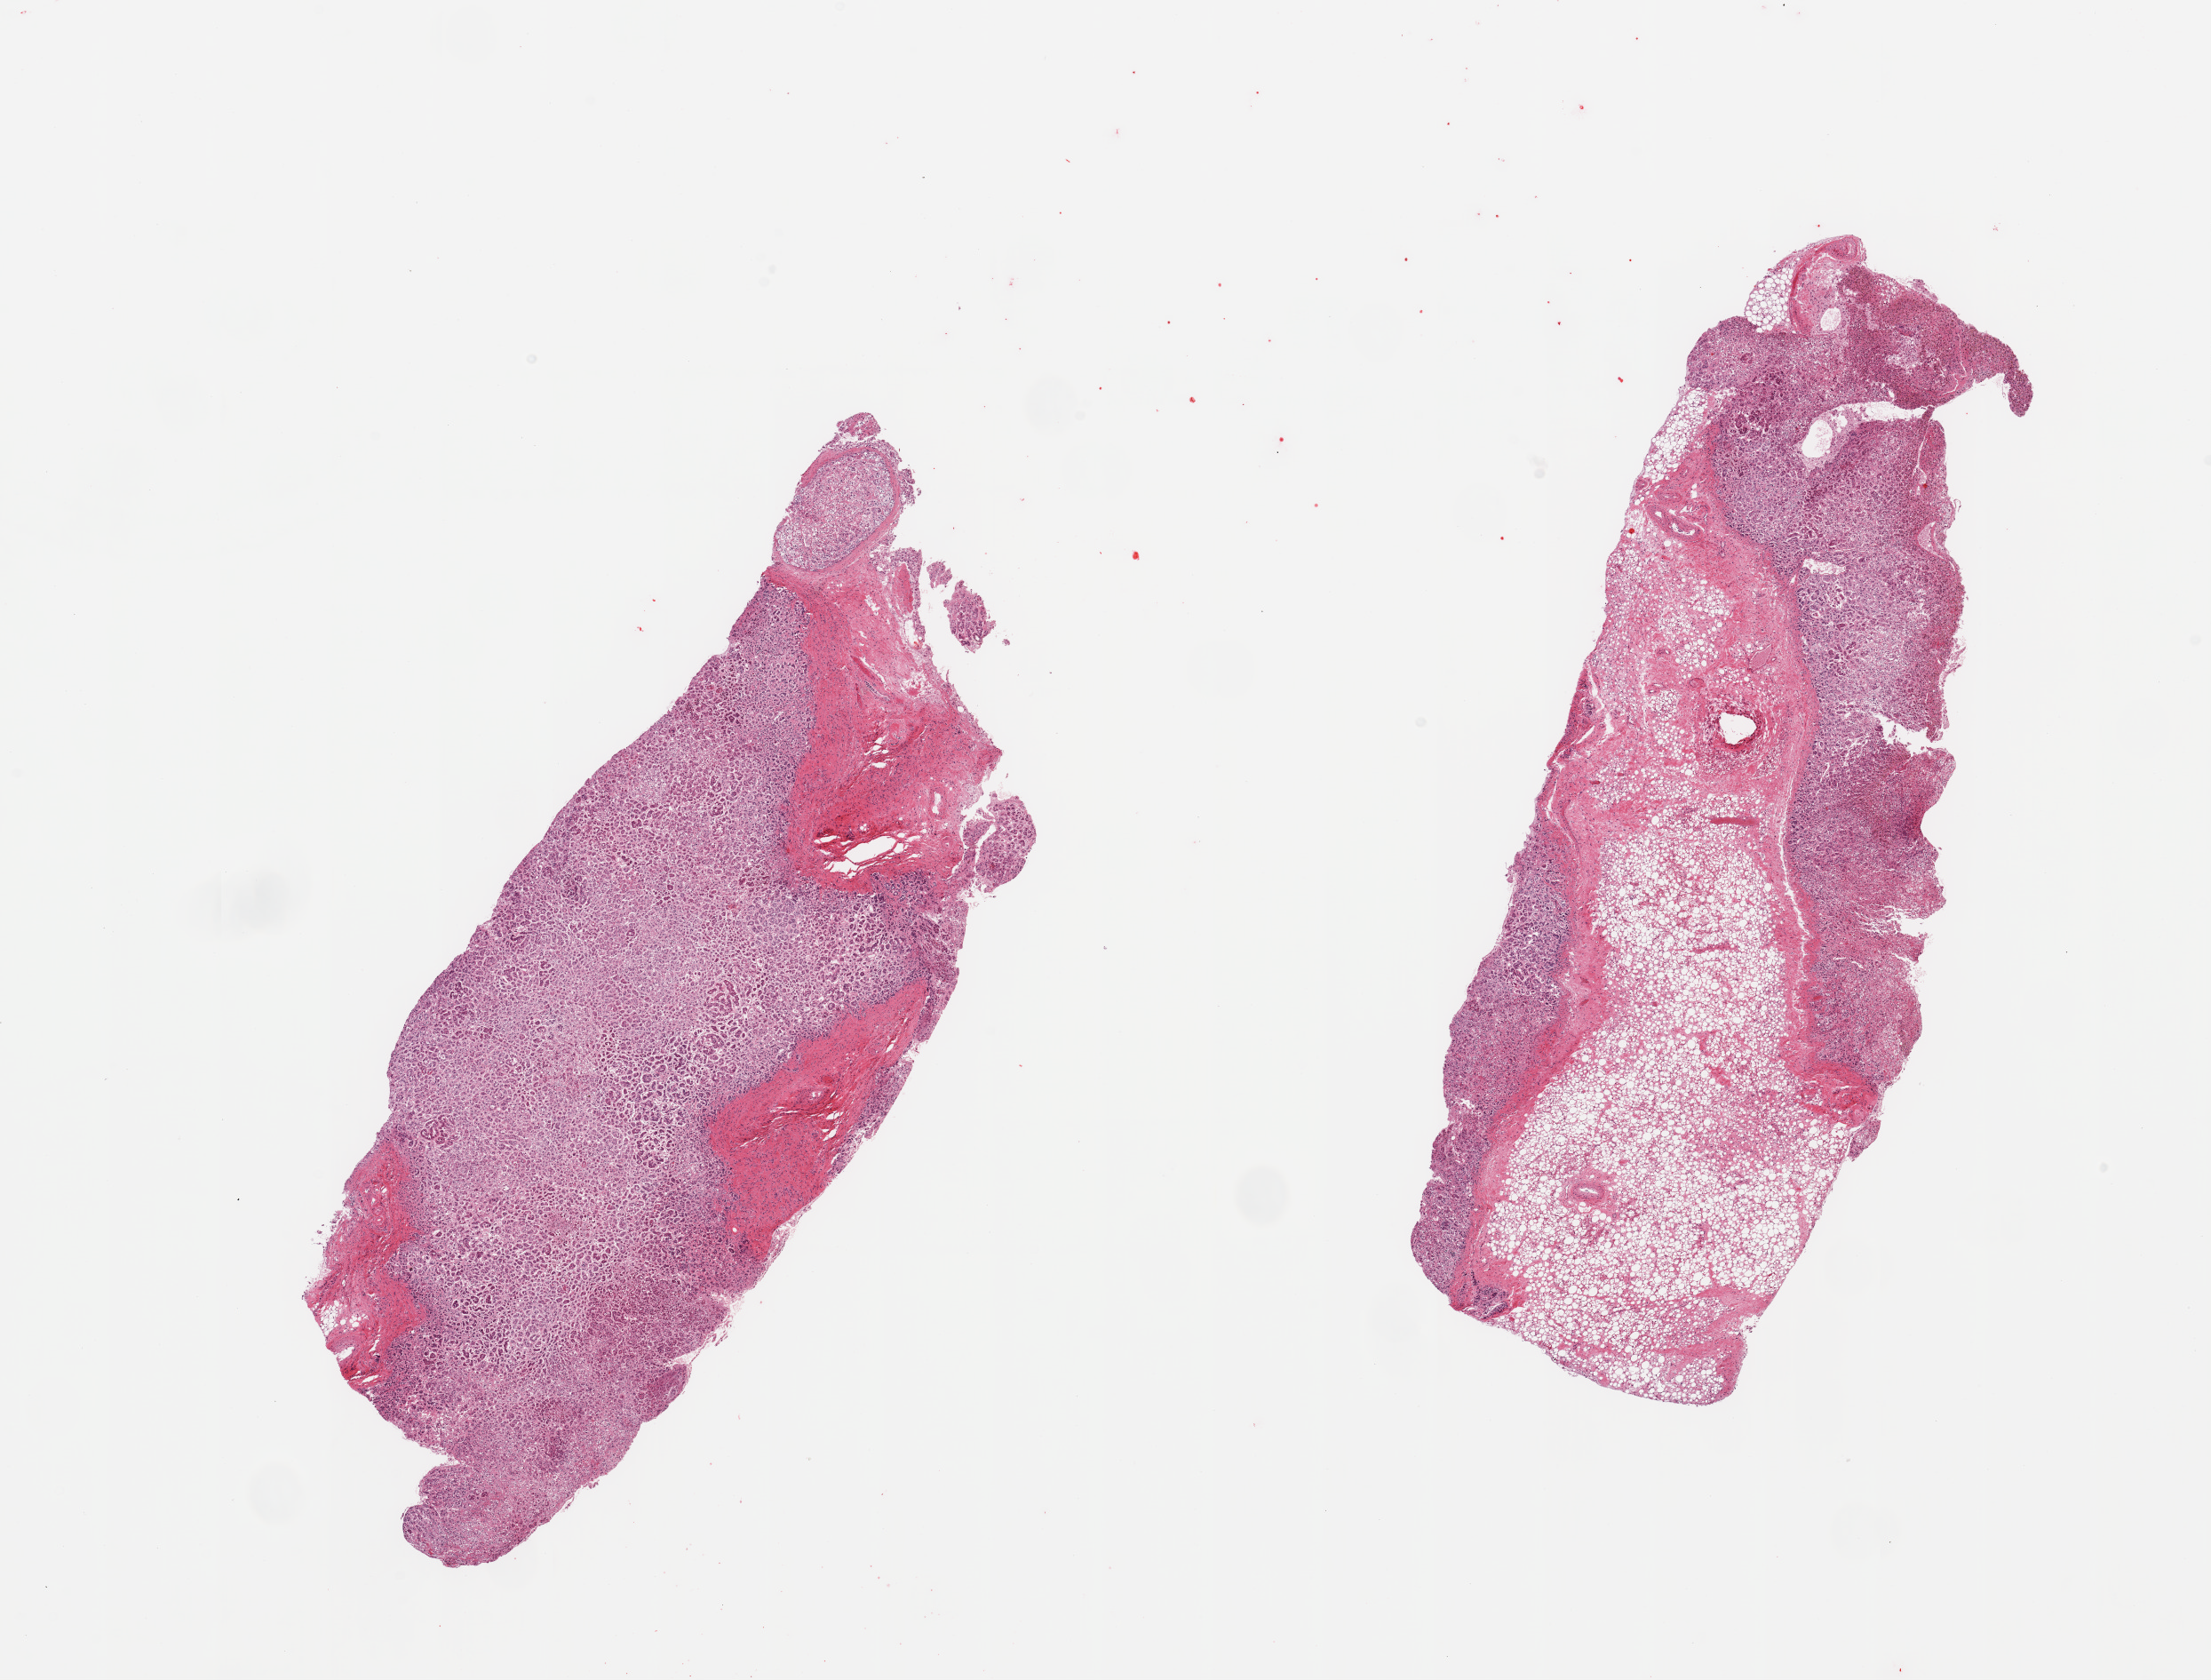
Digitized H&E-stained section, brightfield, shown as a low-resolution overview of the whole scanned area (about 19.7 x 15.0 mm, slide scanned at 20x); PAXgene-fixed, paraffin-embedded tissue; target tissue: adrenal gland; donor tissue sample. Donor sex: male.
Review note (as recorded): 2 pieces, cortex, ~50% fat/fascia.